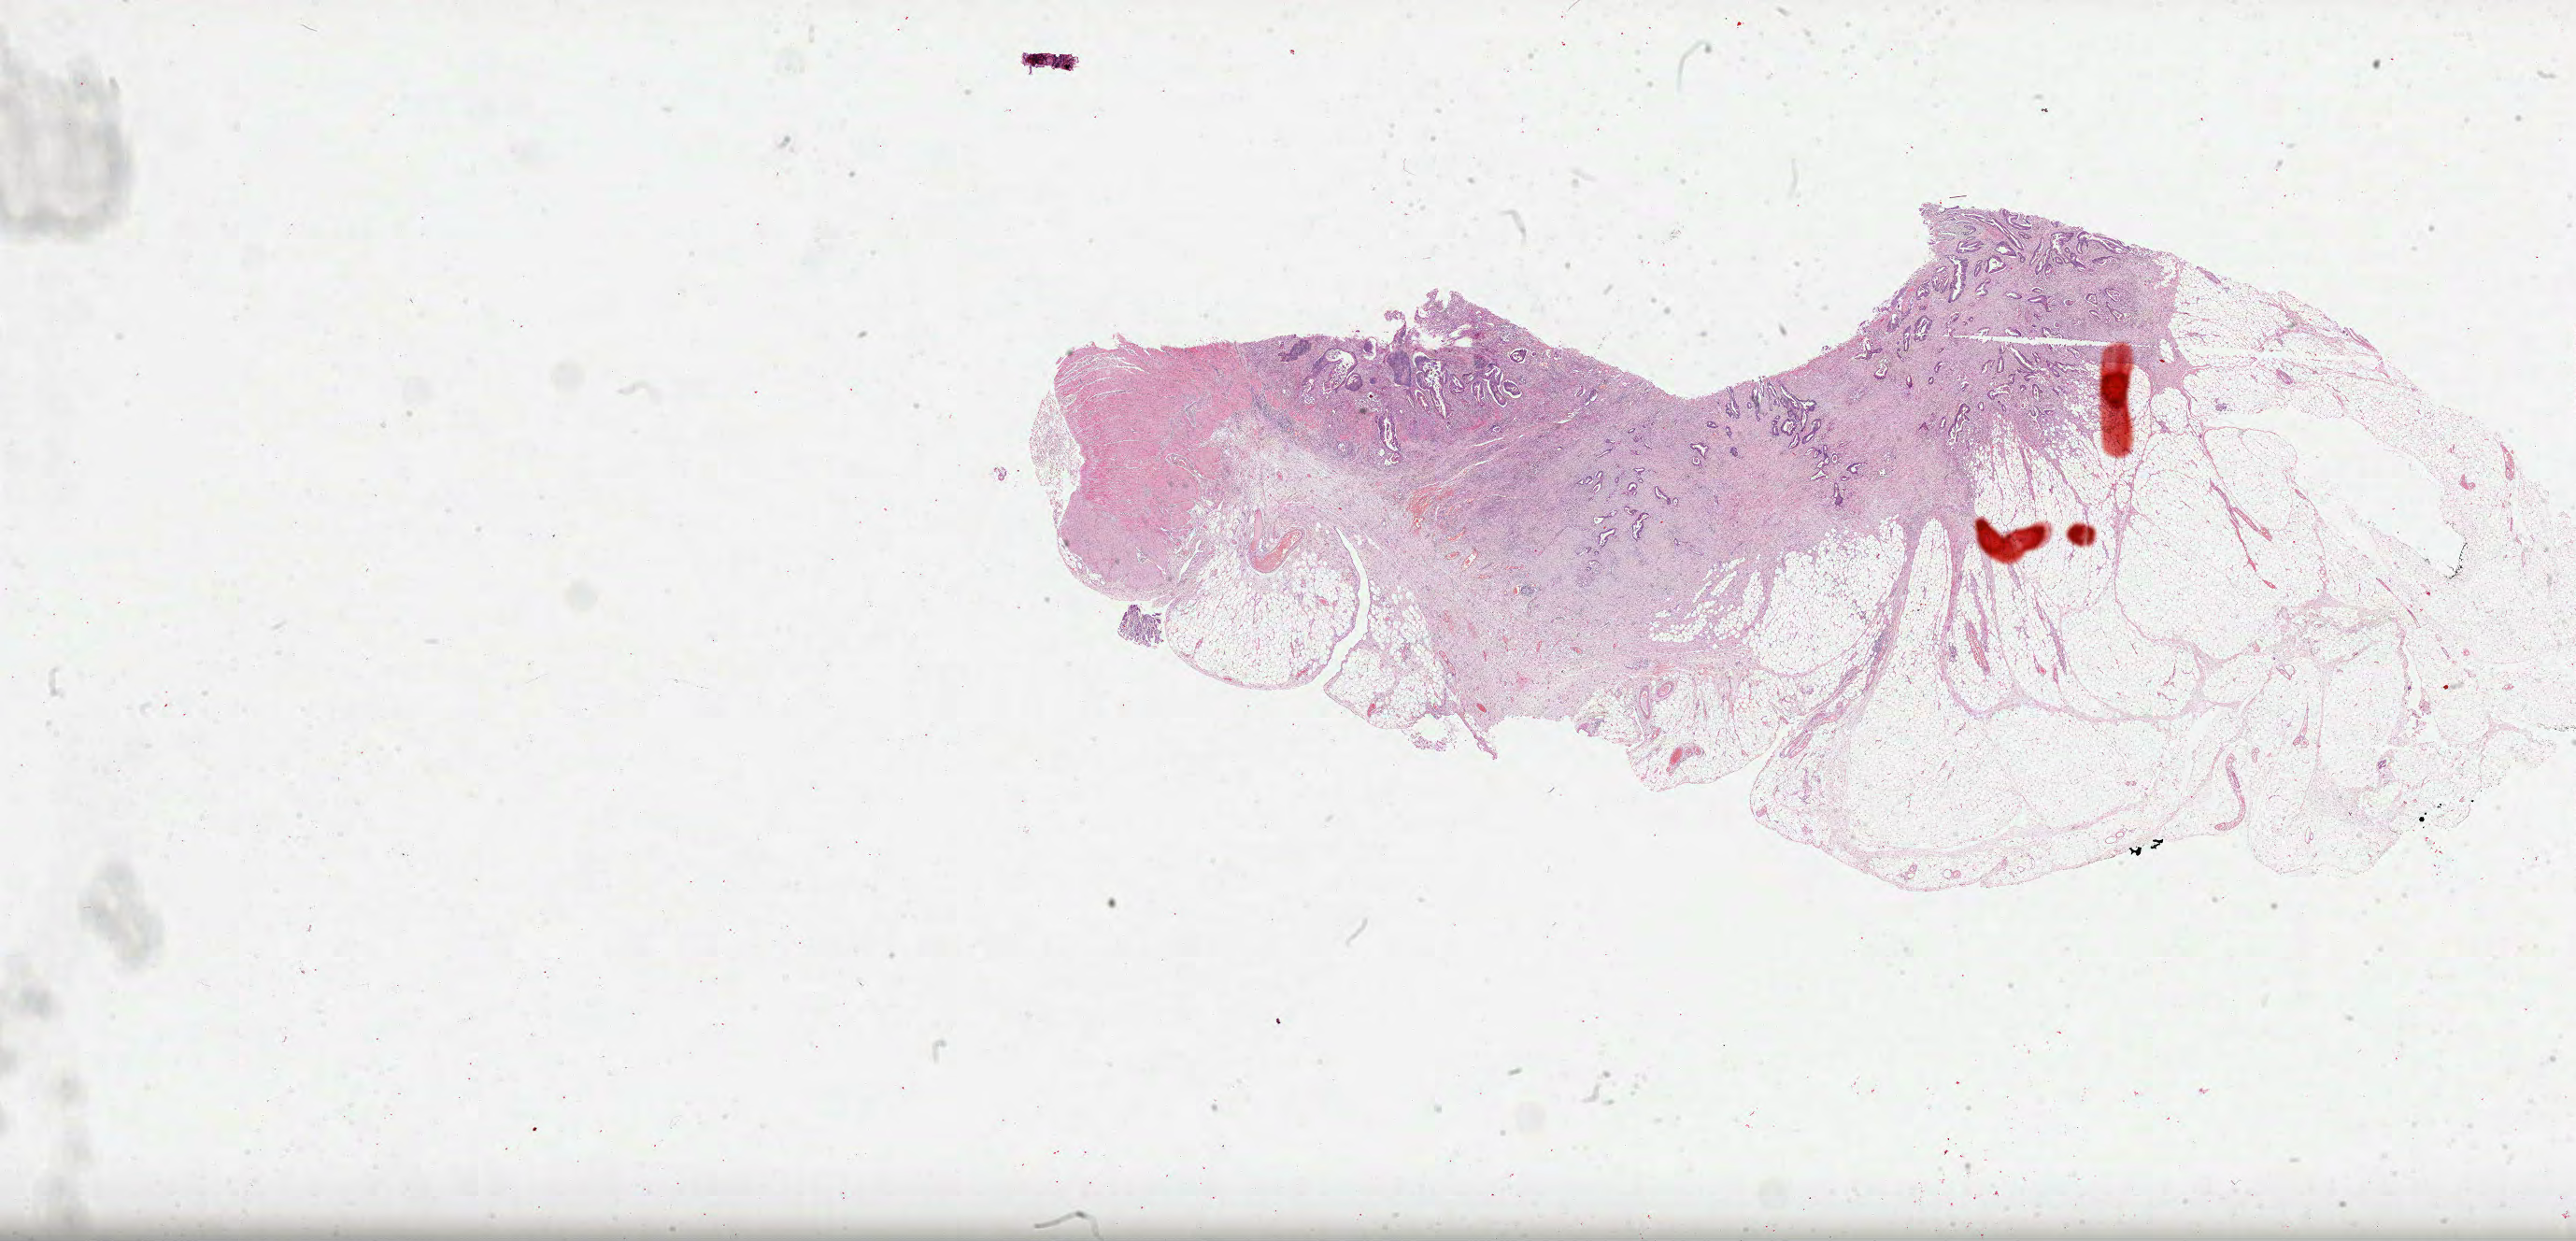
Digitized H&E tissue section (whole slide), whole scanned area (about 44.5 x 21.4 mm) shown as a low-resolution overview, FFPE section, sample: primary tumour, colon. Patient: female, age at initial diagnosis 45 years.
• histologic diagnosis: Adenocarcinoma, NOS (transverse colon)
• lymph nodes positive (case pathology): 0 of 12 examined